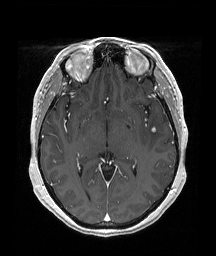
Brain MRI from a brain-tumour surgery series, one axial slice. Position 108 of 192 along the scan axis. T1-weighted post-contrast. 216 × 256 image matrix, field of view 211 × 250 mm. Case-level facts recorded for this patient, not image findings: histopathology: Papillary glioneuronal tumor; WHO grade: 1; tumour location: Left Temporal.
Annotated regions visible in this slice (manually delineated by an expert):
- tumour: bounding box <151,126,156,132> (left, top, right, bottom; pixels)